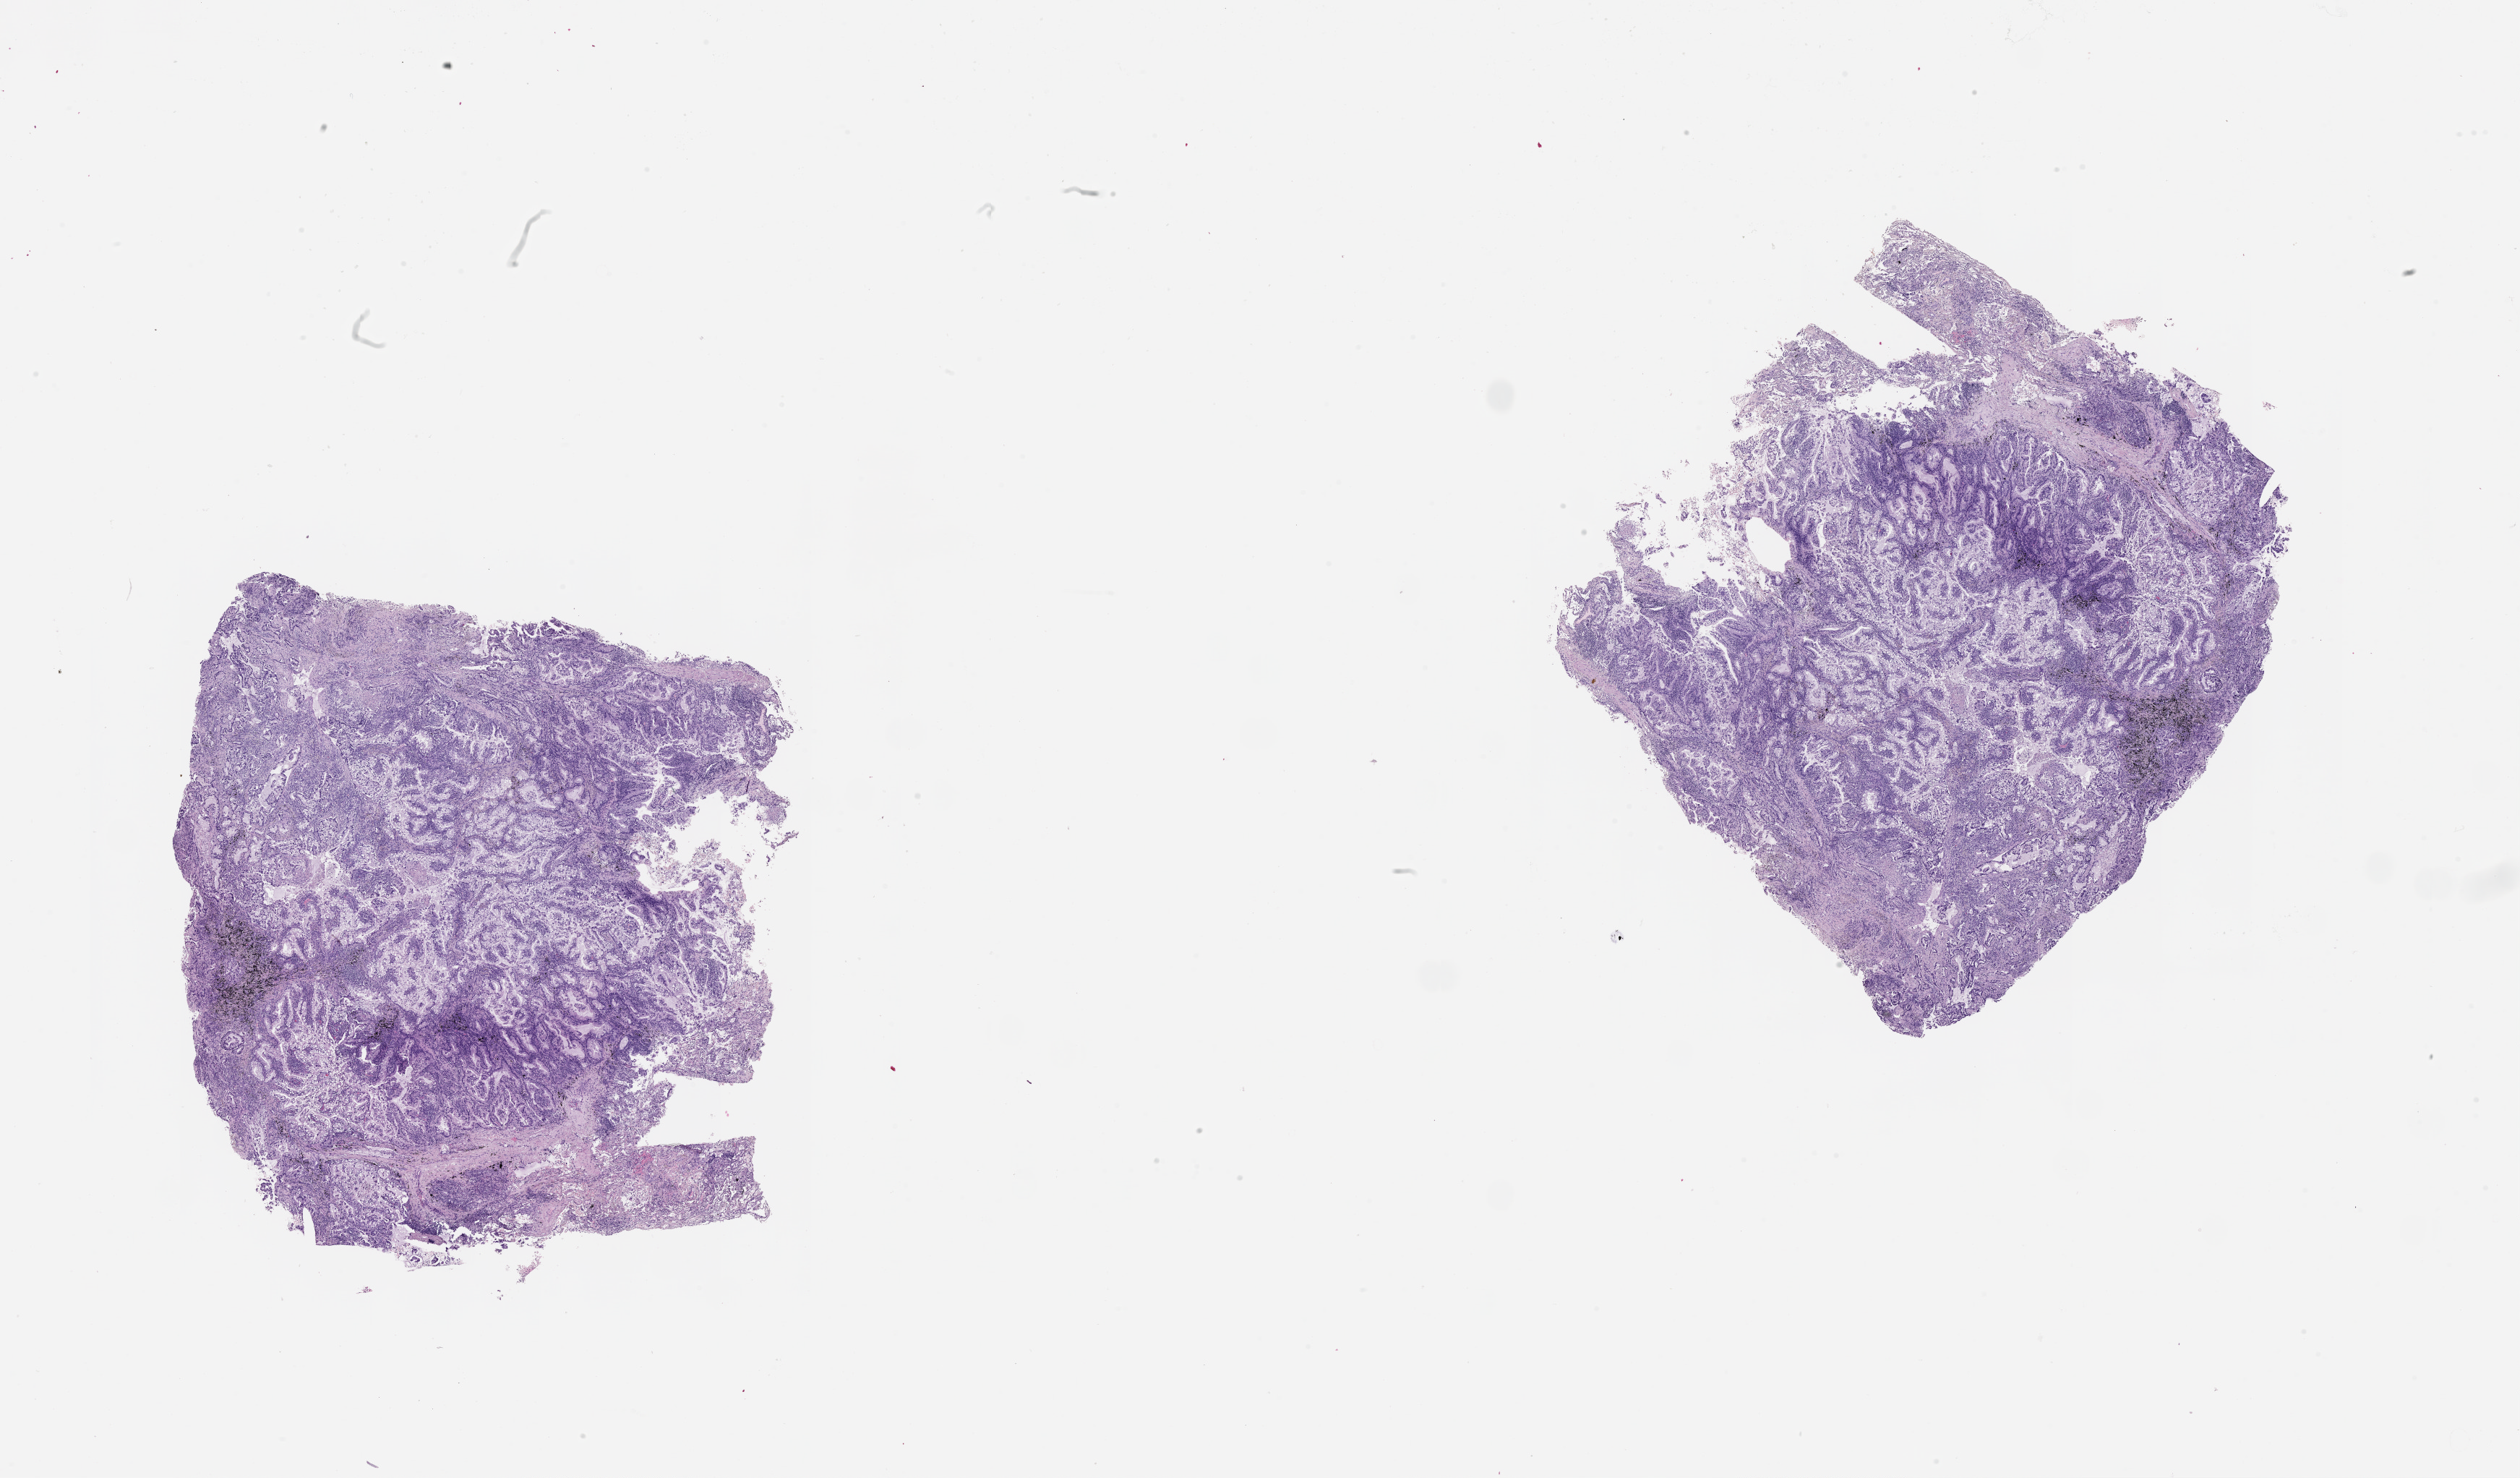
Whole-slide histology image, H&E-stained — whole scanned area (about 28.1 x 16.5 mm, slide scanned at 20x) shown as a low-resolution overview. Lung, tumour tissue. Patient: male, age 67 years. Histologic grade: G2 (moderately differentiated).
AJCC pathologic stage: IA. Histologic diagnosis: Adenocarcinoma, NOS.